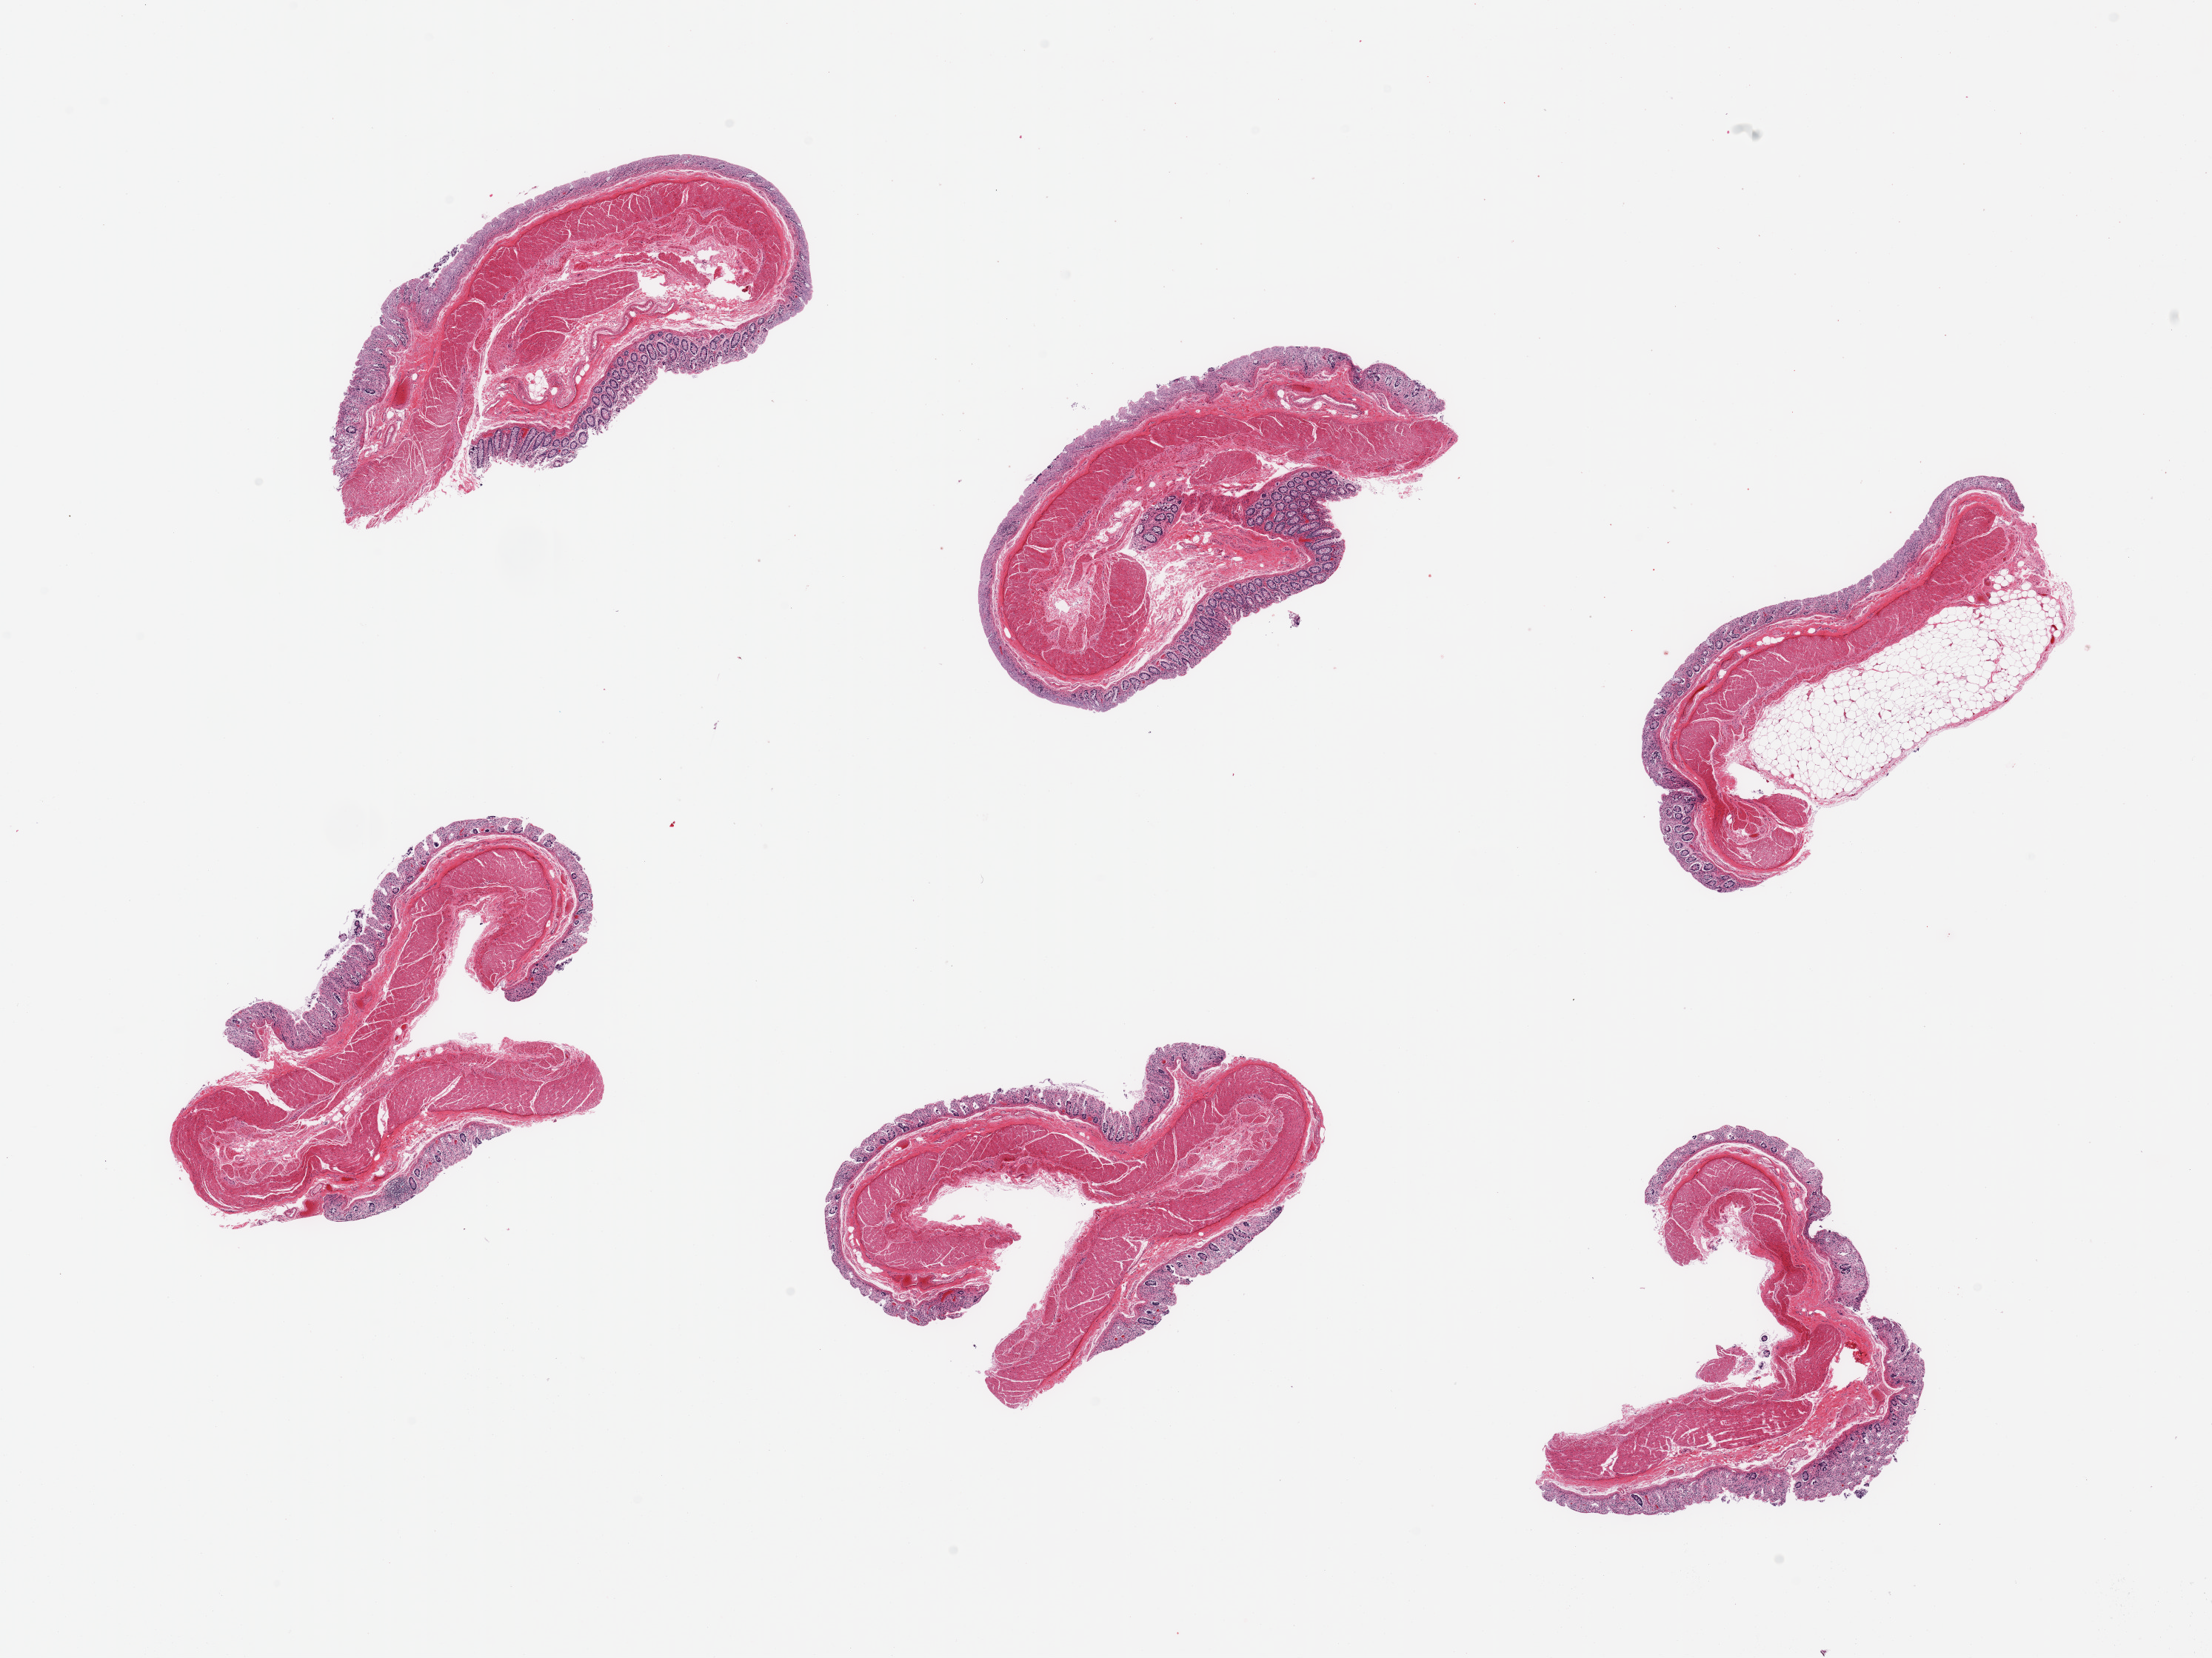
Digitized haematoxylin and eosin-stained section, shown as a low-resolution overview of the whole scanned area (about 23.6 x 17.7 mm), PAXgene-fixed, paraffin-embedded tissue, section of transverse colon (target tissue), donor tissue sample. Female donor.
Review note (as recorded): 6 pieces; full thickness sections, mucosa largely autolyzed.